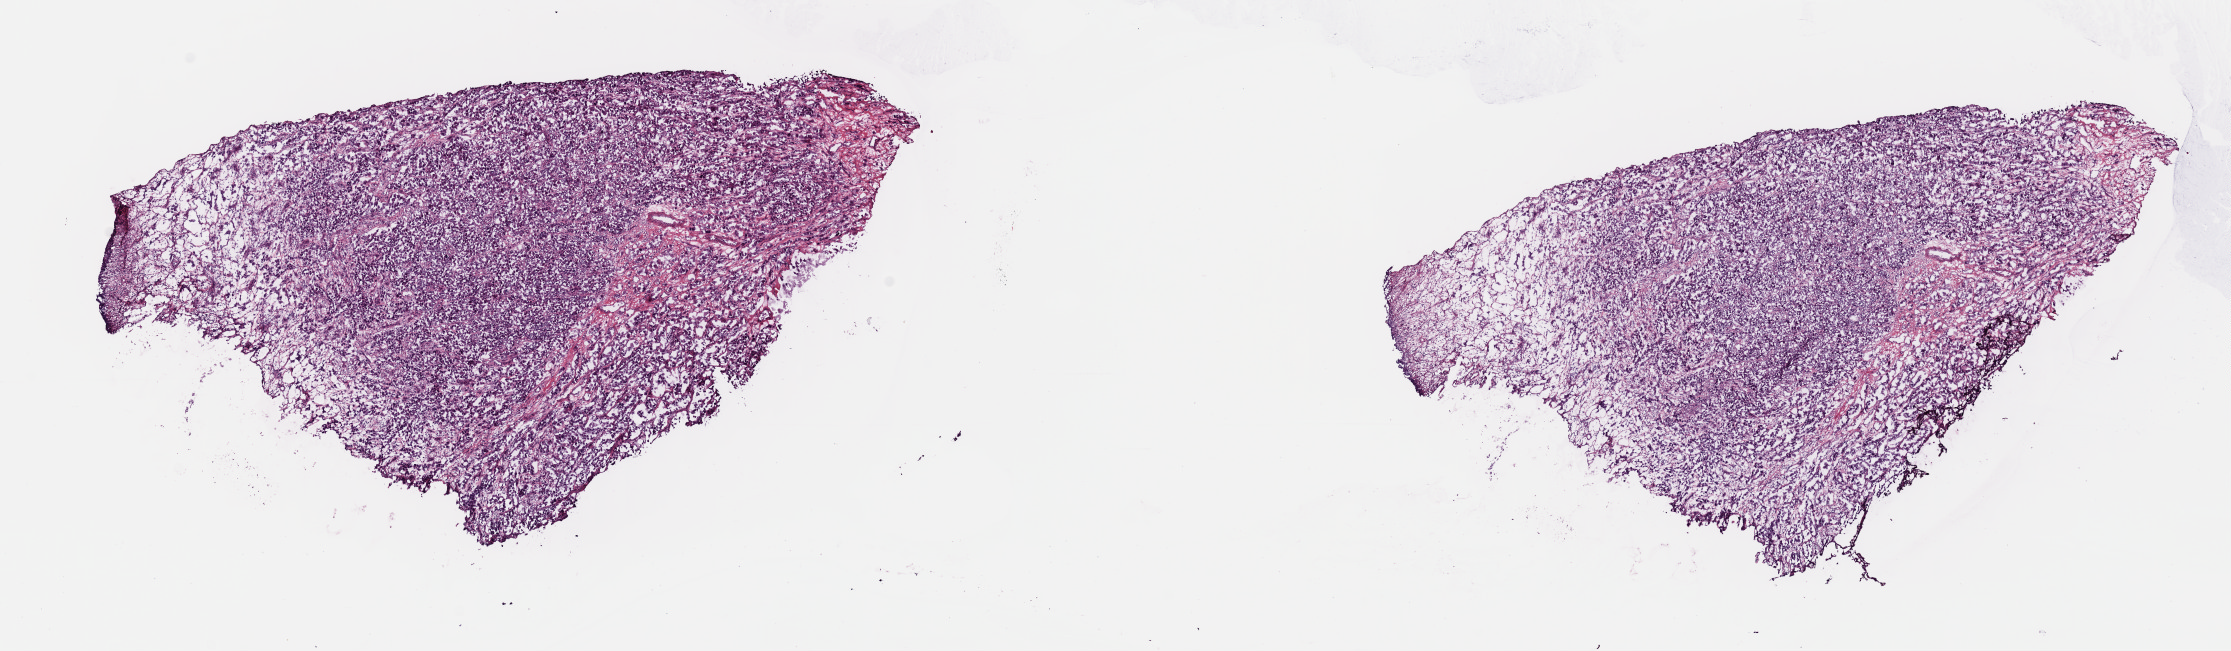
Whole-slide histology image, H&E, whole scanned area (about 17.6 x 5.1 mm, slide scanned at 40x) shown as a low-resolution overview, frozen section from the top of the tissue portion, metastatic tumour sample, sampled site: connective, subcutaneous and other soft tissues of lower limb and hip. Female patient; age at initial diagnosis 58 years. Pathologist review of this section (percent, as recorded): tumour cells 95%, tumour nuclei 90%, normal cells 0%, stromal cells 5%, necrosis 0%. Infiltration values recorded for this section: lymphocyte infiltration 0%, monocyte infiltration 0%, neutrophil infiltration 0%.
• this section: metastatic tumour tissue
• patient diagnosis: Malignant melanoma, NOS